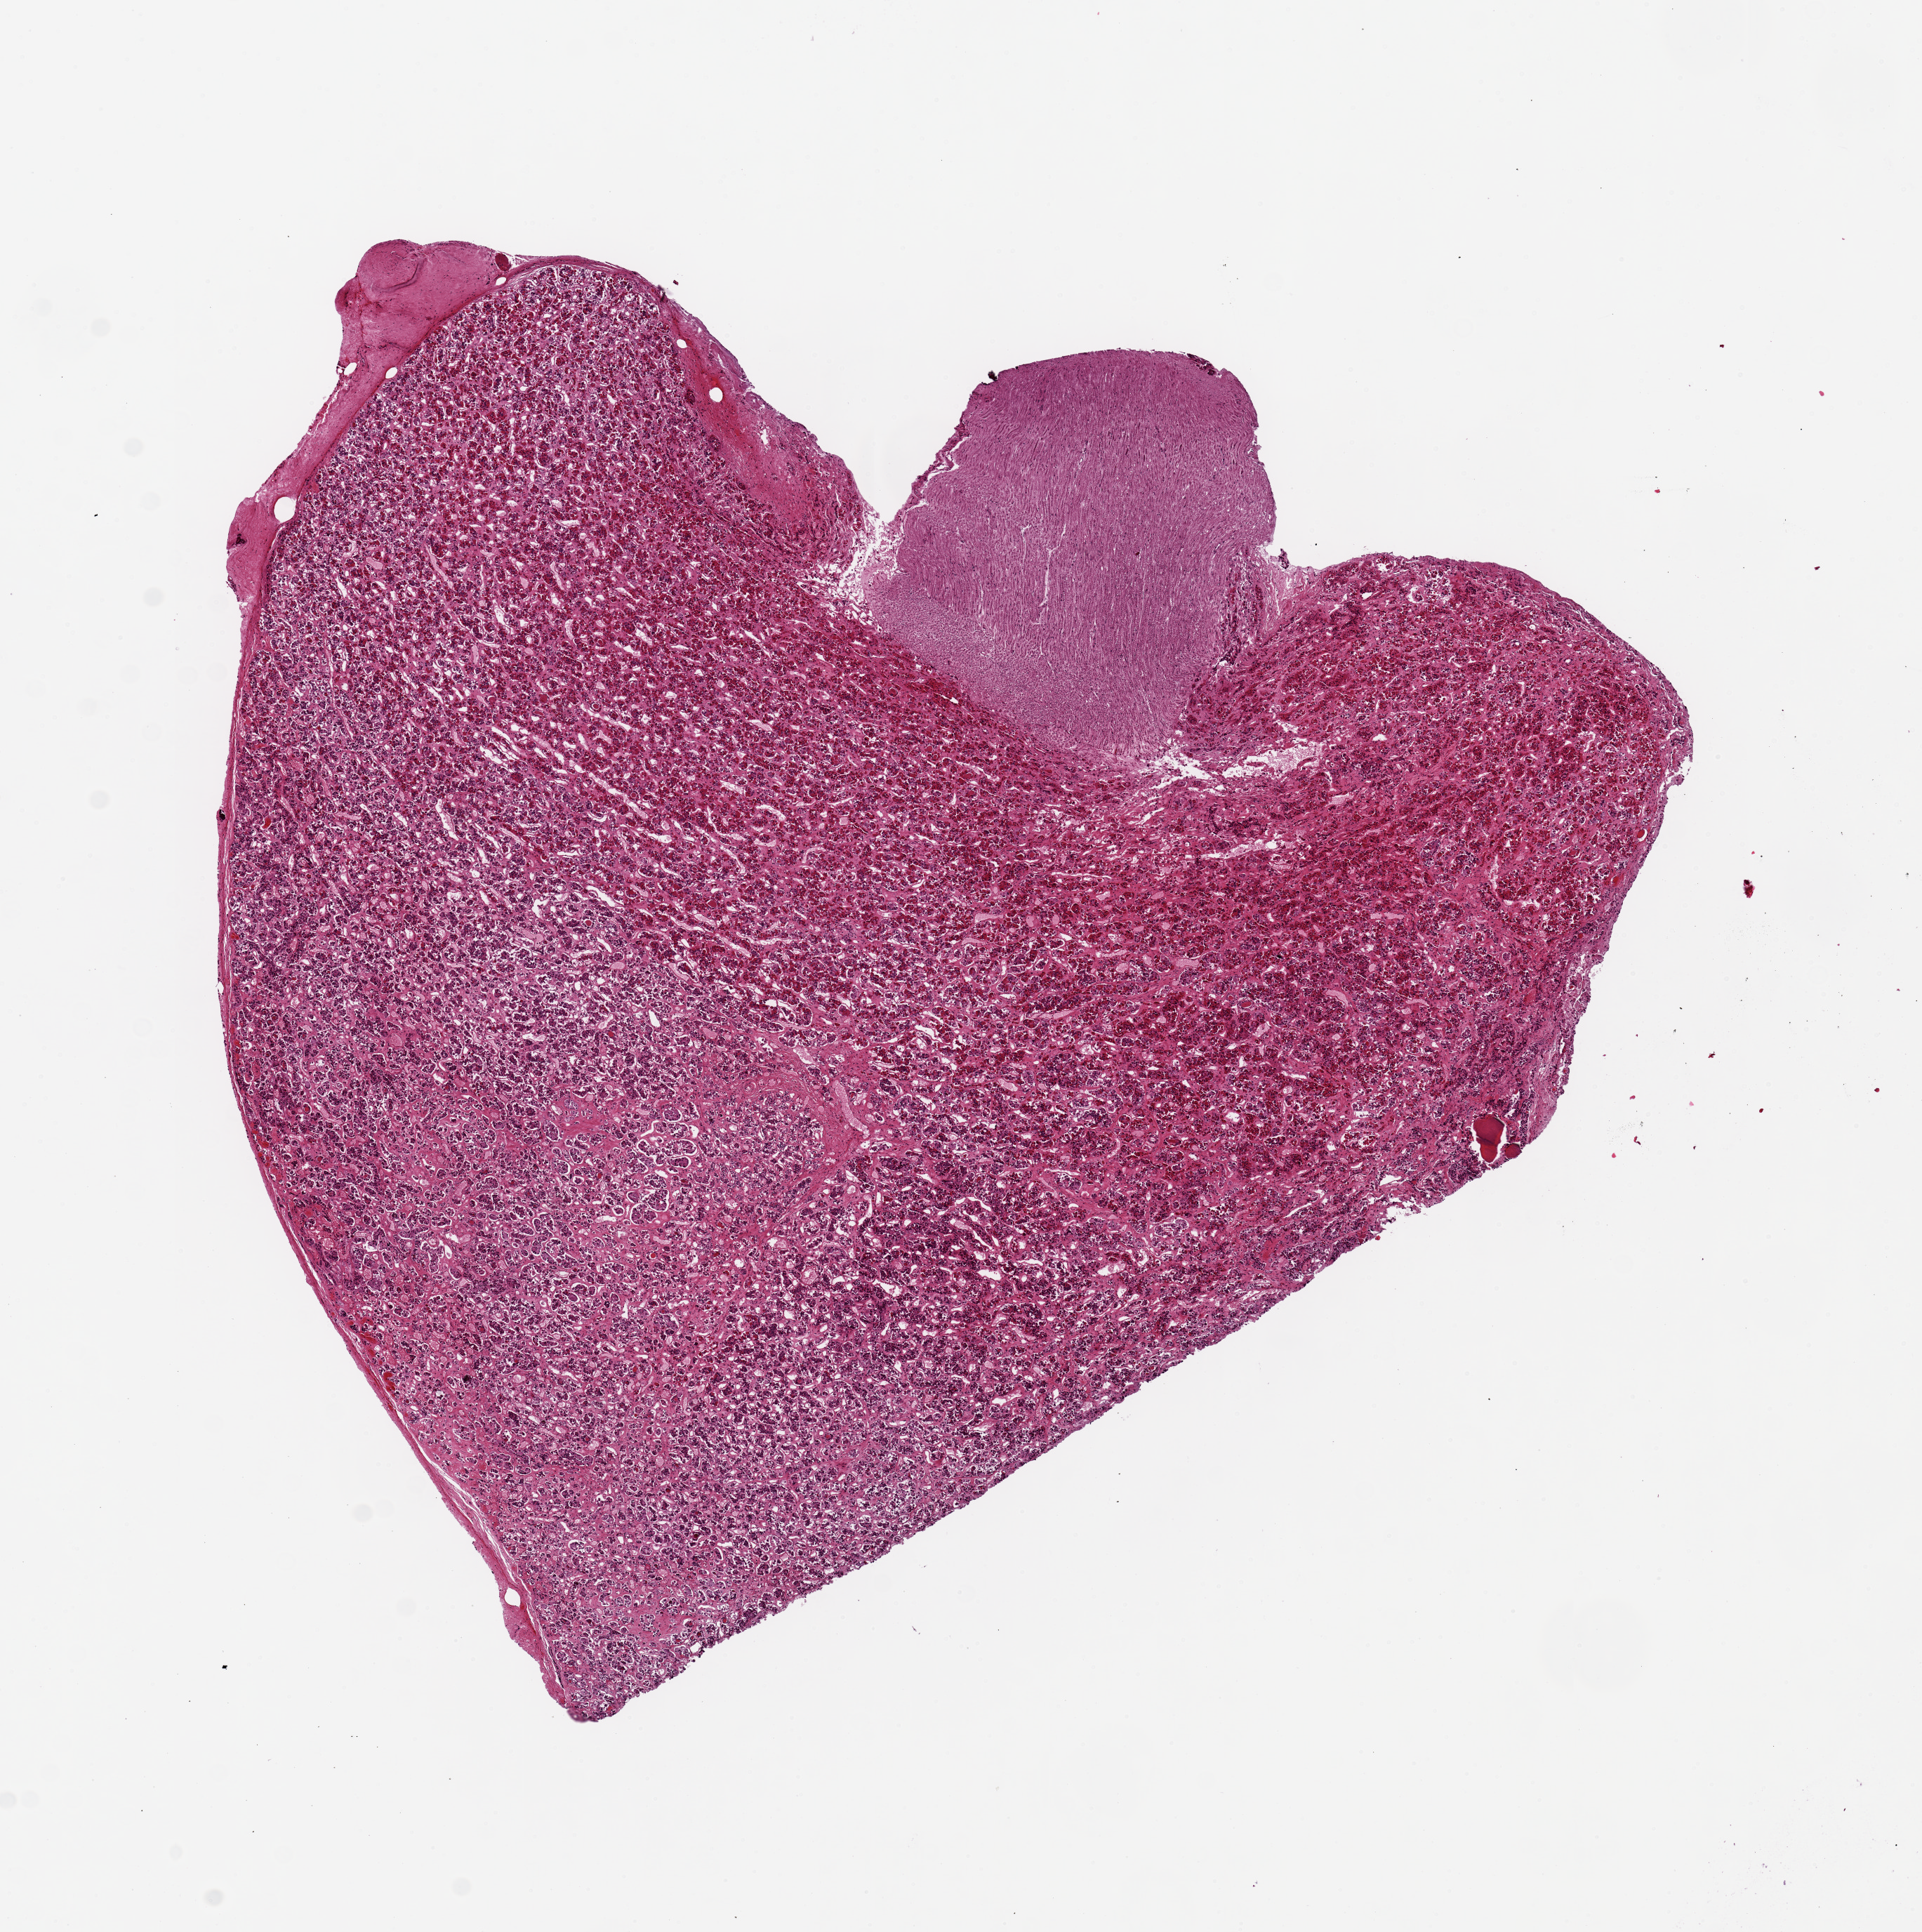
Whole-slide image, hematoxylin and eosin (H&E) stain, brightfield — shown as a low-resolution overview of the whole scanned area (about 10.8 x 10.9 mm); PAXgene-fixed paraffin-embedded (PFPE) section; sampled site (target tissue): pituitary; donor tissue sample. Donor: male.
Pathologist's review note for this sample: 1 piece, 8x8mm; Mostly anterior pit.; 2x2 mm posterior pituitary.